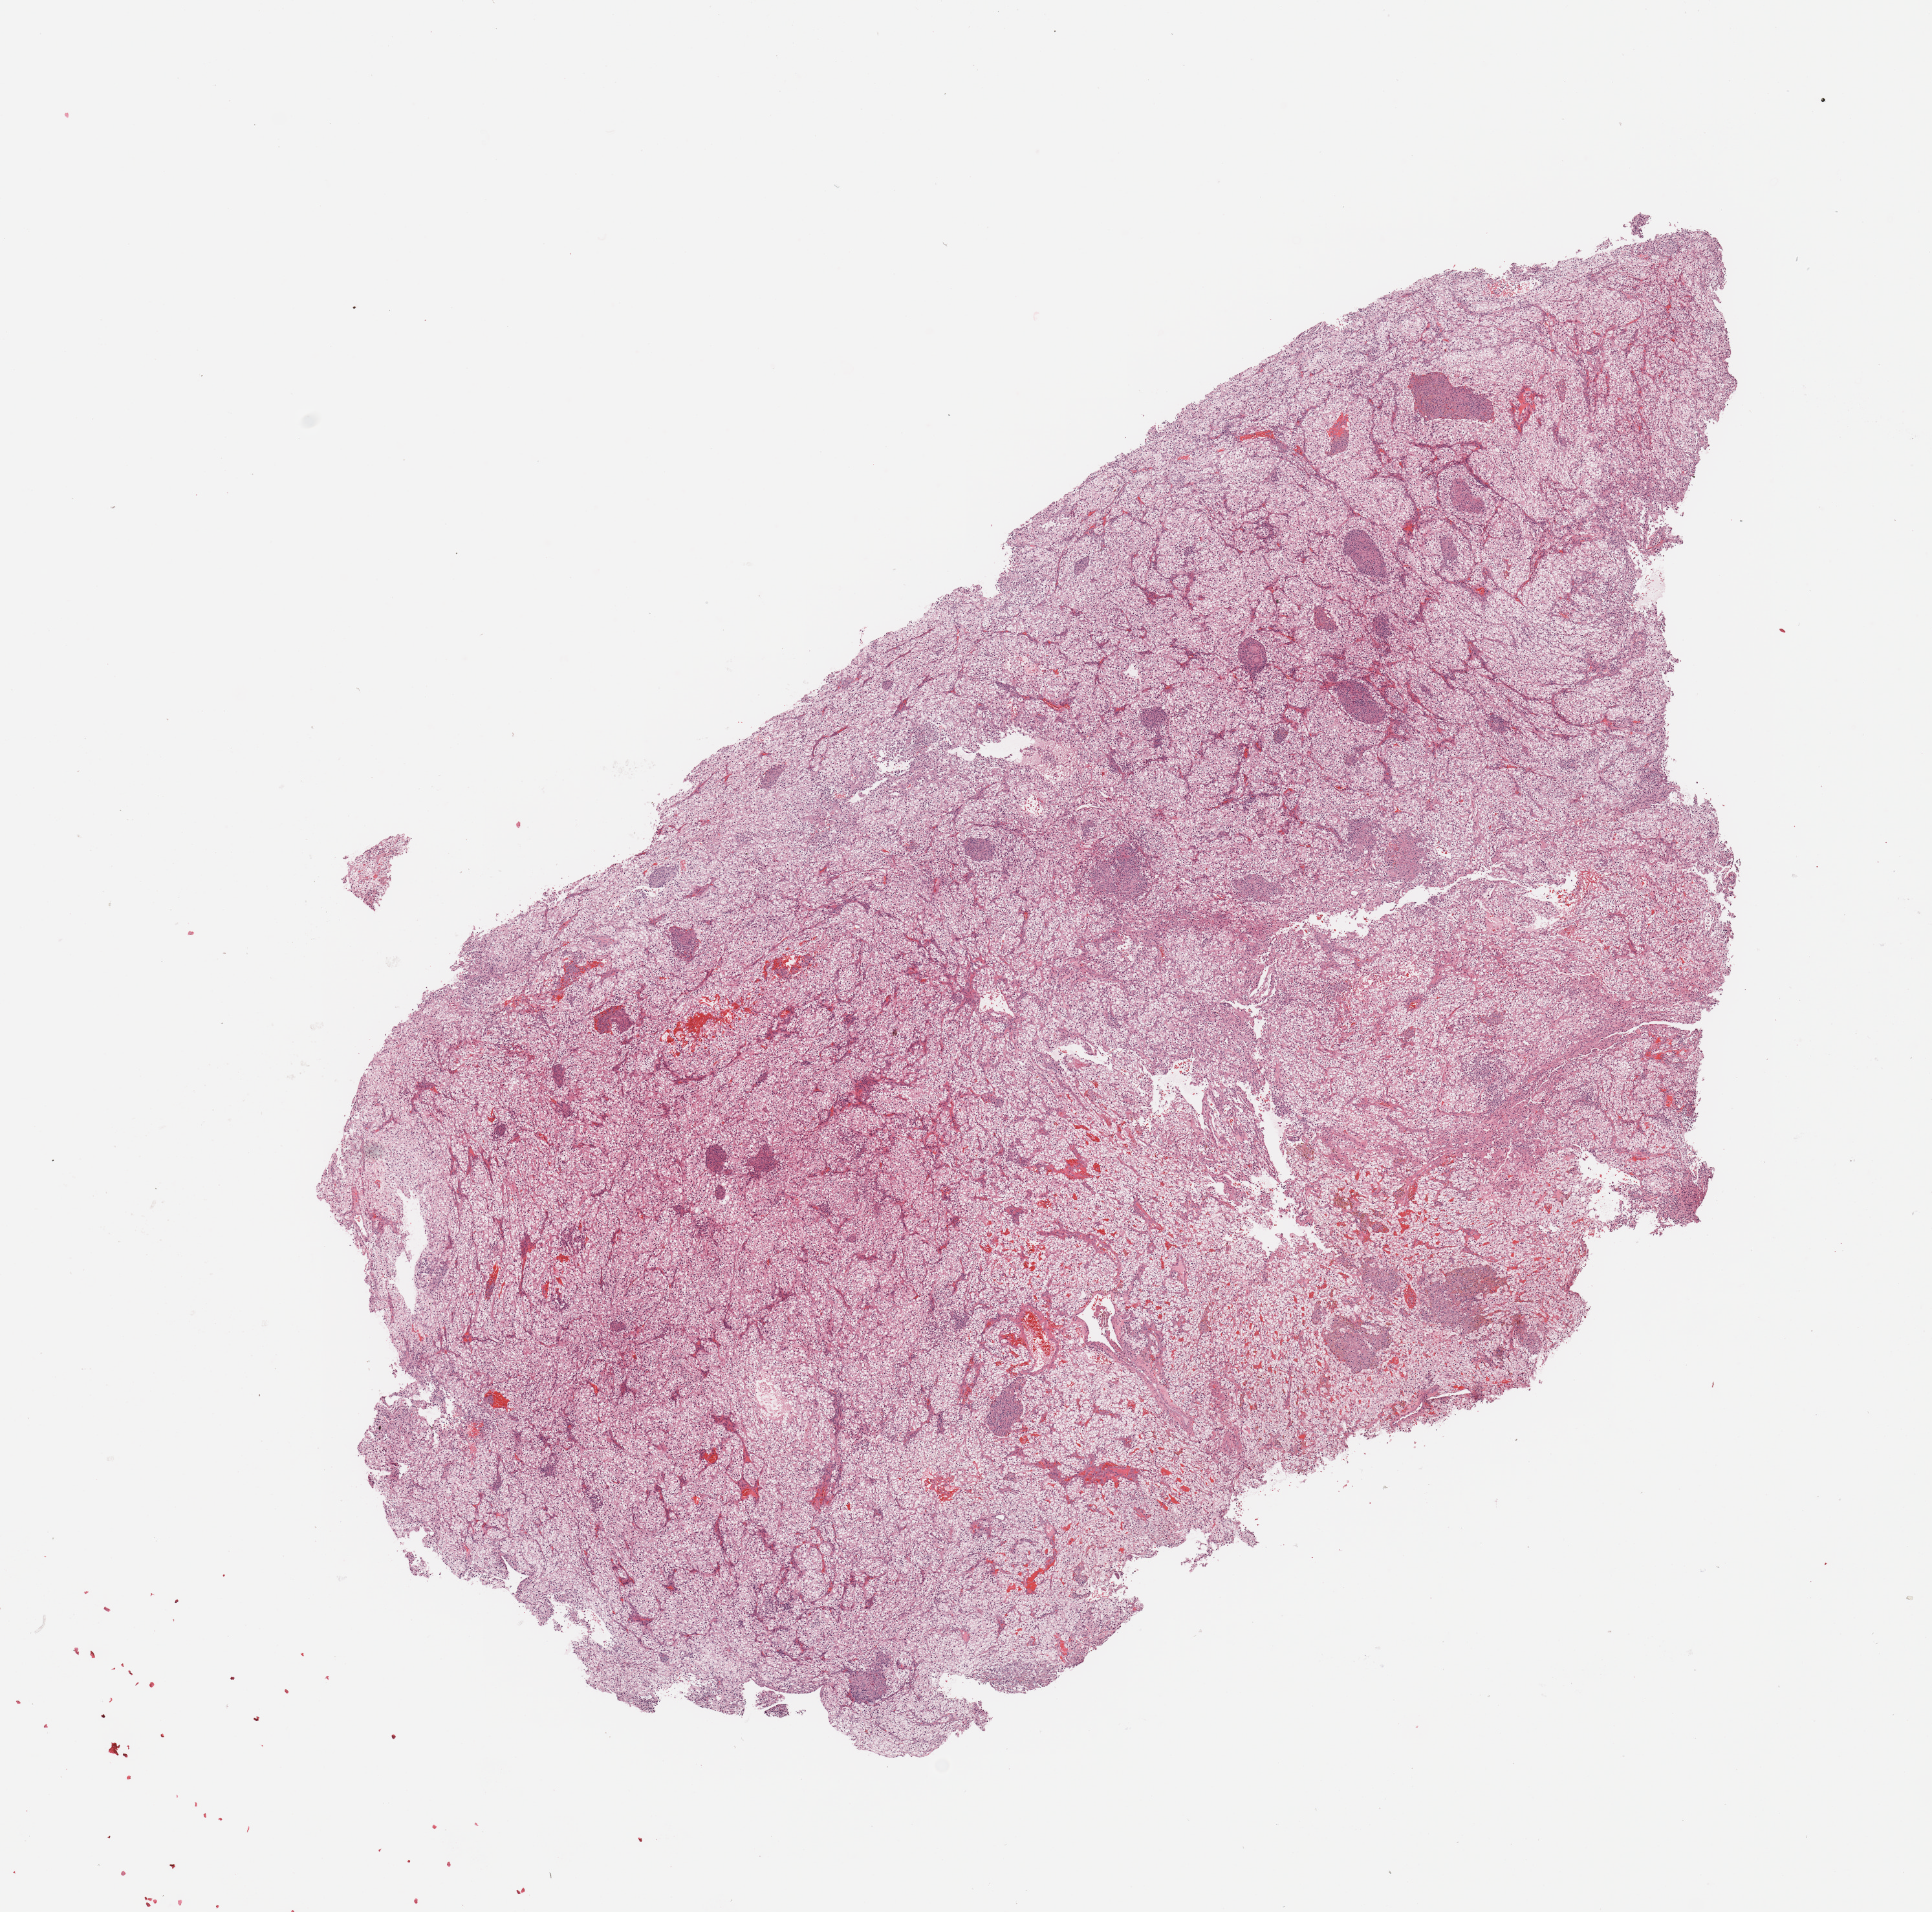
Digitized H&E tissue section (whole slide) — a low-resolution overview of the entire scanned area, about 11.8 x 11.7 mm (from a 20x scan), tumour tissue sample, sampled site: kidney. Patient: male, age 66 years. Histologic grade: G3 (poorly differentiated). Slide review estimates, as recorded: tumour nuclei 95%, necrosis 5%.
• AJCC pathologic stage: III
• diagnosis: Renal cell carcinoma, NOS
• primary tumour site (as recorded): middle